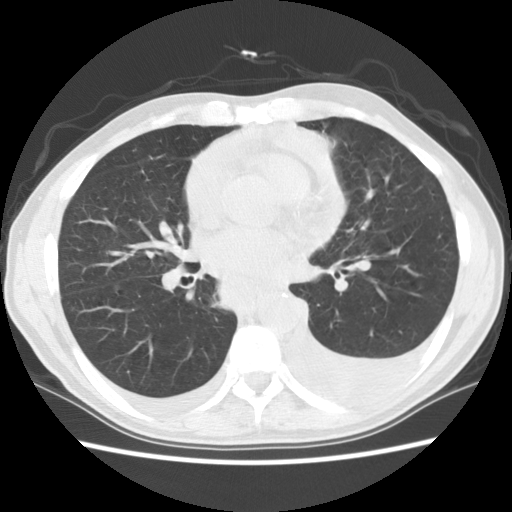
Axial slice from a low-dose chest CT screening exam, baseline annual screen, lung window (W 1500 / L -600 HU), 2.5 mm slice thickness, slice 63 of 135 in the series. Male, age 60 years at enrolment. Current smoker at enrolment.
Expert-annotated lung lesion, bounding box (x1, y1, x2, y2) in pixels: (173, 242, 307, 335). No non-calcified nodule or mass ≥4 mm was recorded by the screening reader at this exam. Official screen result: negative screen, significant abnormalities not suspicious for lung cancer.